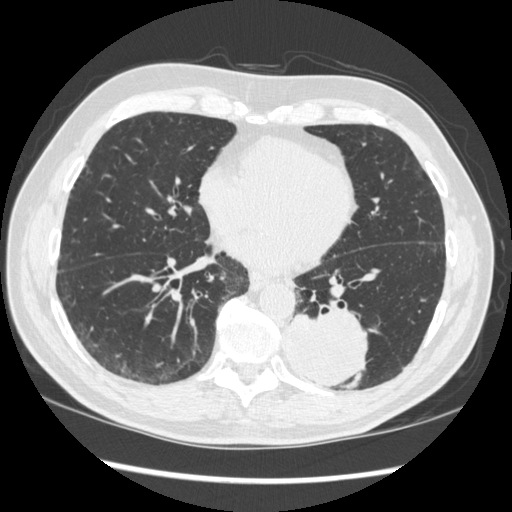
Low-dose screening chest CT, one axial slice; position 130 of 348 along the scan axis; reconstruction kernel STANDARD; 120 kVp; lung window (W 1500 / L -600 HU); 1.25 mm slice thickness; 512 × 512 image matrix, field of view 360 × 360 mm.
Structures marked on this image (outlined manually by an expert reader):
- lesion 1 (tumor, lower lobe of left lung): bounding box <284,311,368,389> (left, top, right, bottom; pixels)